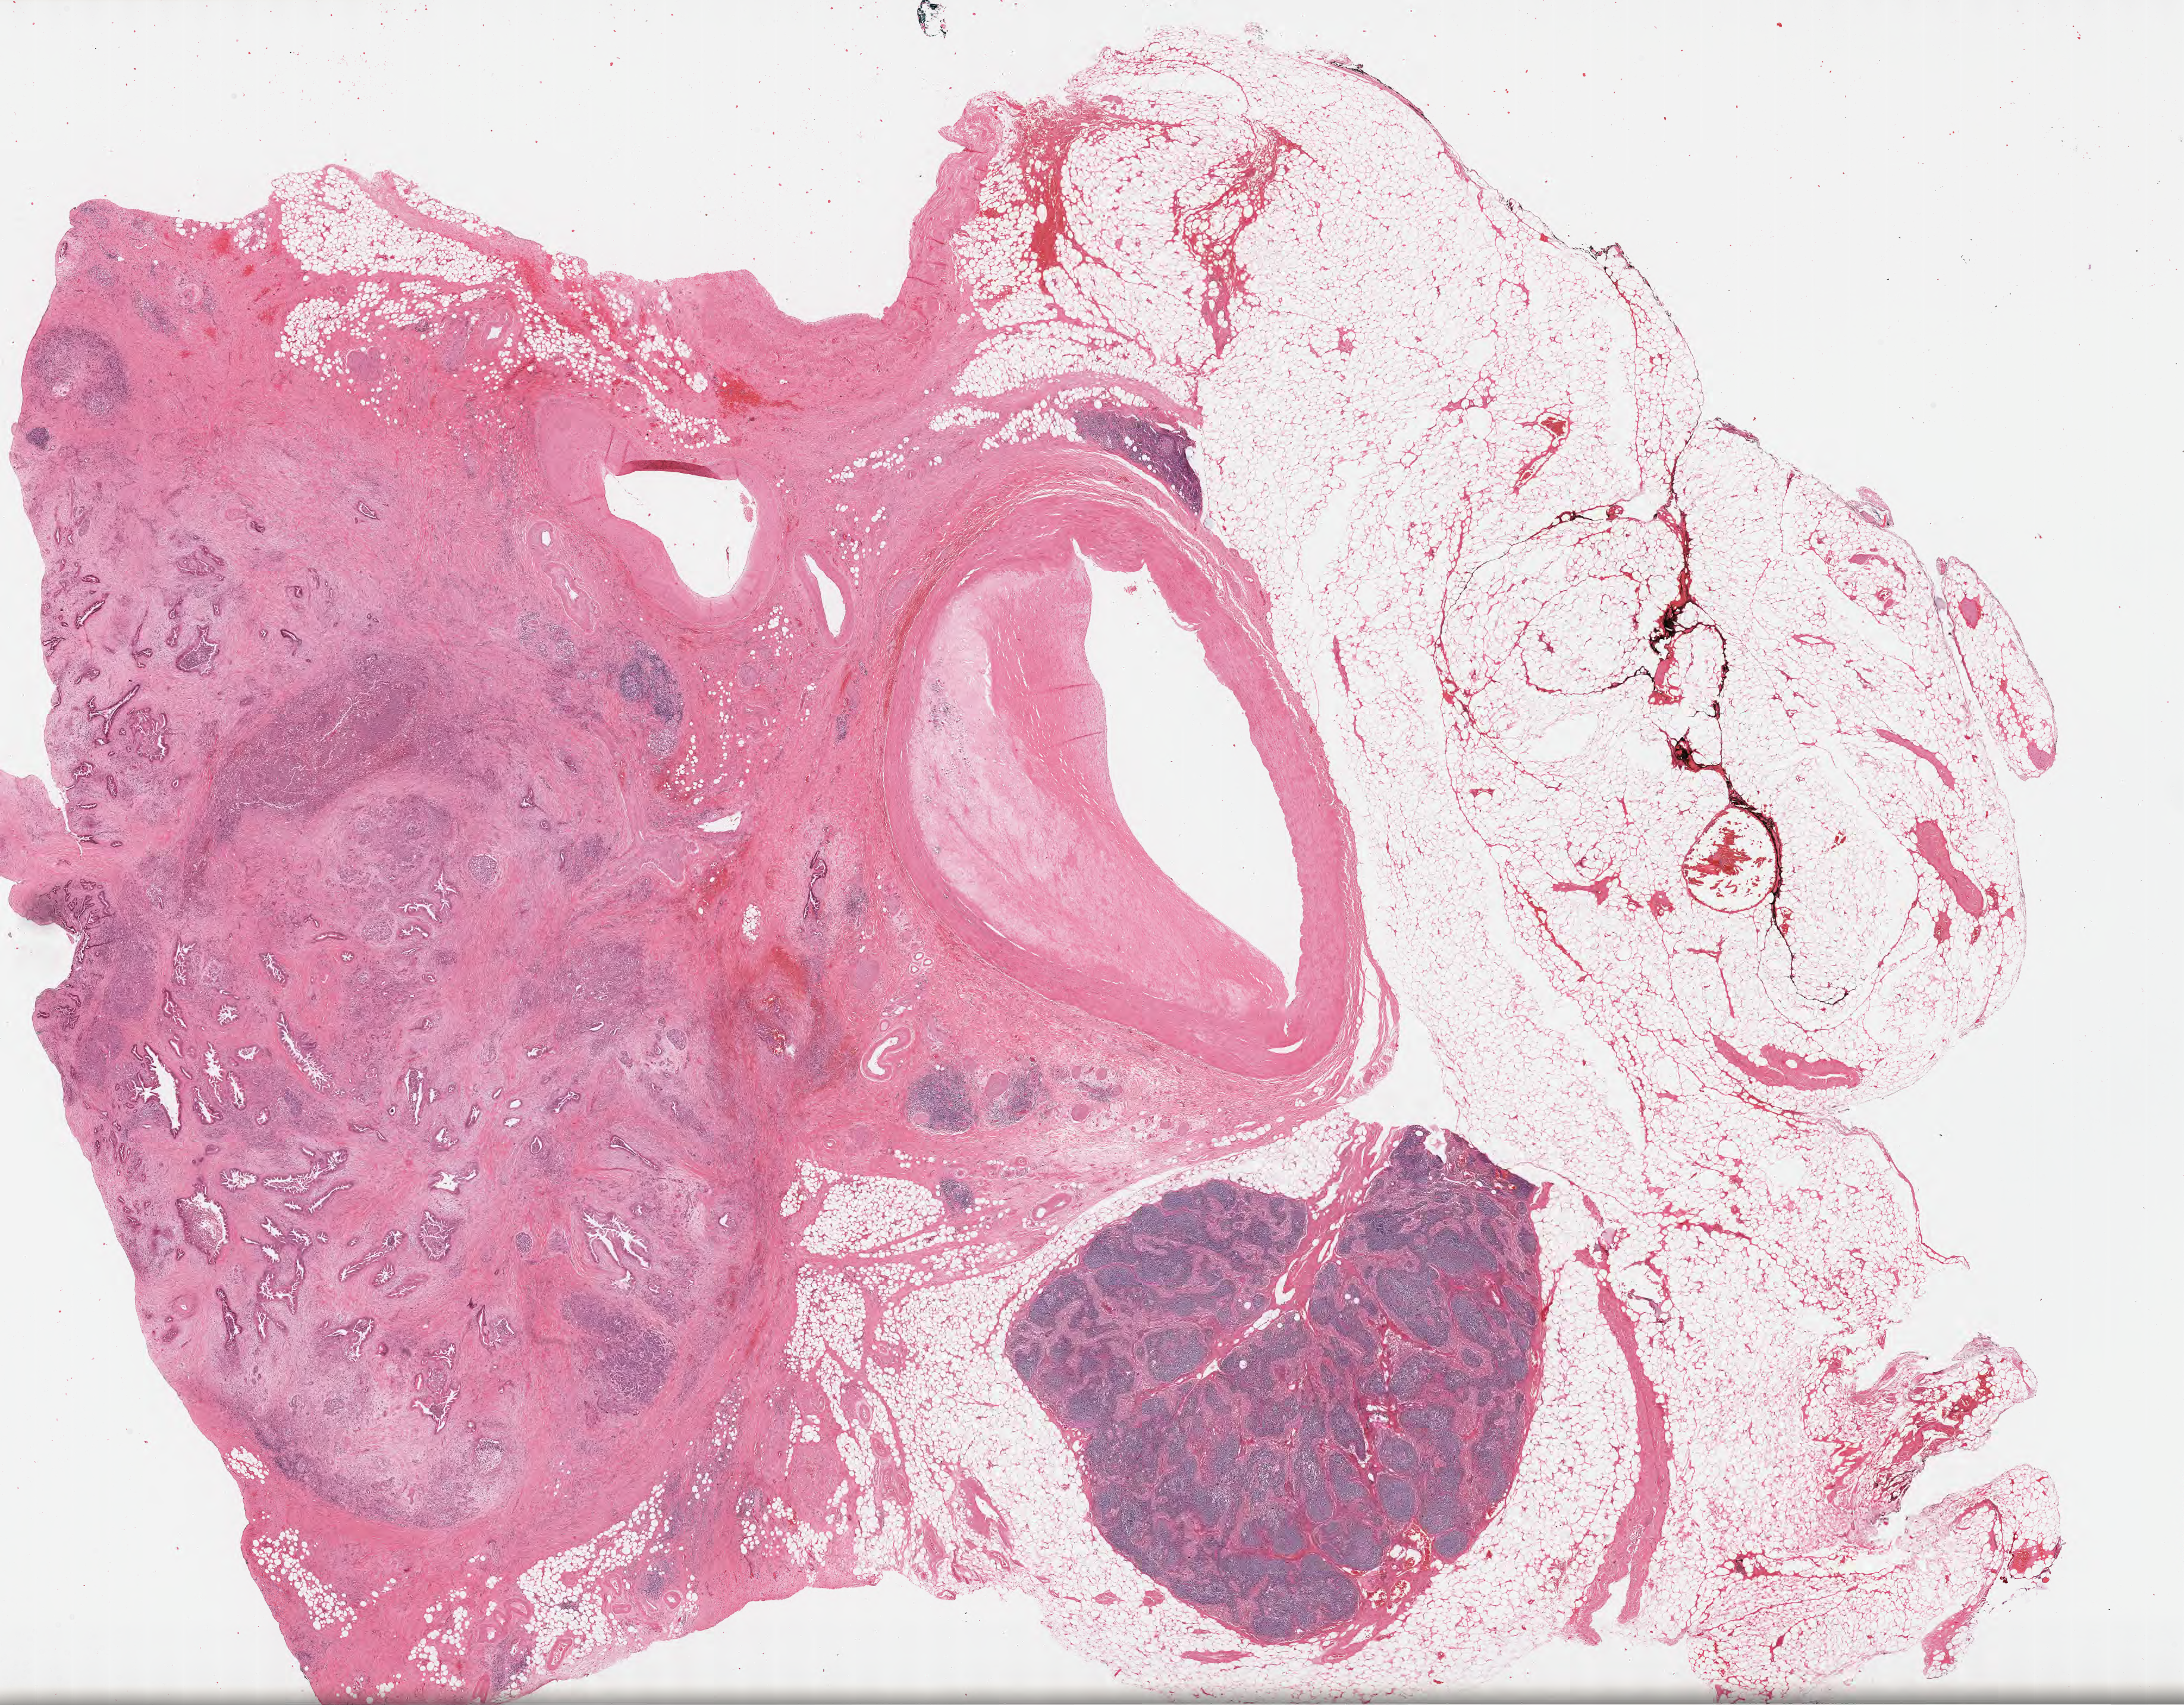
Whole-slide image, hematoxylin and eosin (H&E) stain, whole scanned area (about 29.7 x 23.2 mm) shown as a low-resolution overview, formalin-fixed paraffin-embedded section, primary tumor, site: body of pancreas. Male, age 80 years at initial diagnosis. Tumor grade: G1 (well differentiated). Pathologist review of this section (percent, as recorded): tumor cells 25%, tumor nuclei 25%, stromal cells 70%, necrosis 0%, normal cells 5%. Infiltration values recorded for this section: lymphocyte infiltration 18%, monocyte infiltration 8%, neutrophil infiltration 26%.
* histologic diagnosis: Adenocarcinoma, NOS
* section: top of the tissue portion